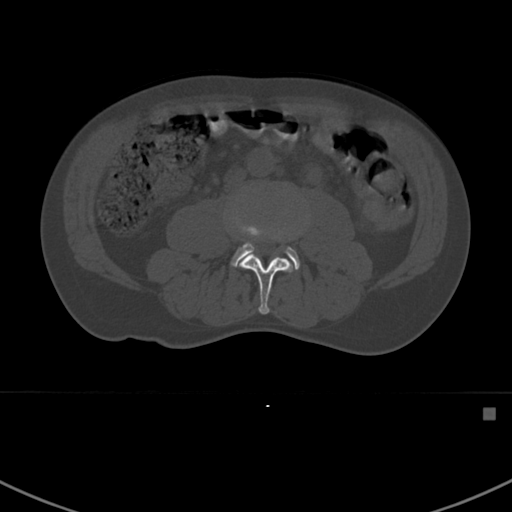
CT including the spine, one axial slice. Position 255 of 412 along the scan axis. Reconstruction kernel Br40s. Bone window (W 1800 / L 400 HU). 1.5 mm slice thickness. 512 × 512 image matrix, field of view 358 × 358 mm. Patient: male, 59 years. Case-level facts recorded for this patient, not image findings: primary cancer: prostate.
Structures marked on this image (semi-automatically segmented with operator editing):
- L3 vertebra: bounding box <239,236,293,314> (left, top, right, bottom; pixels)
- L4 vertebra: <231,211,300,270>